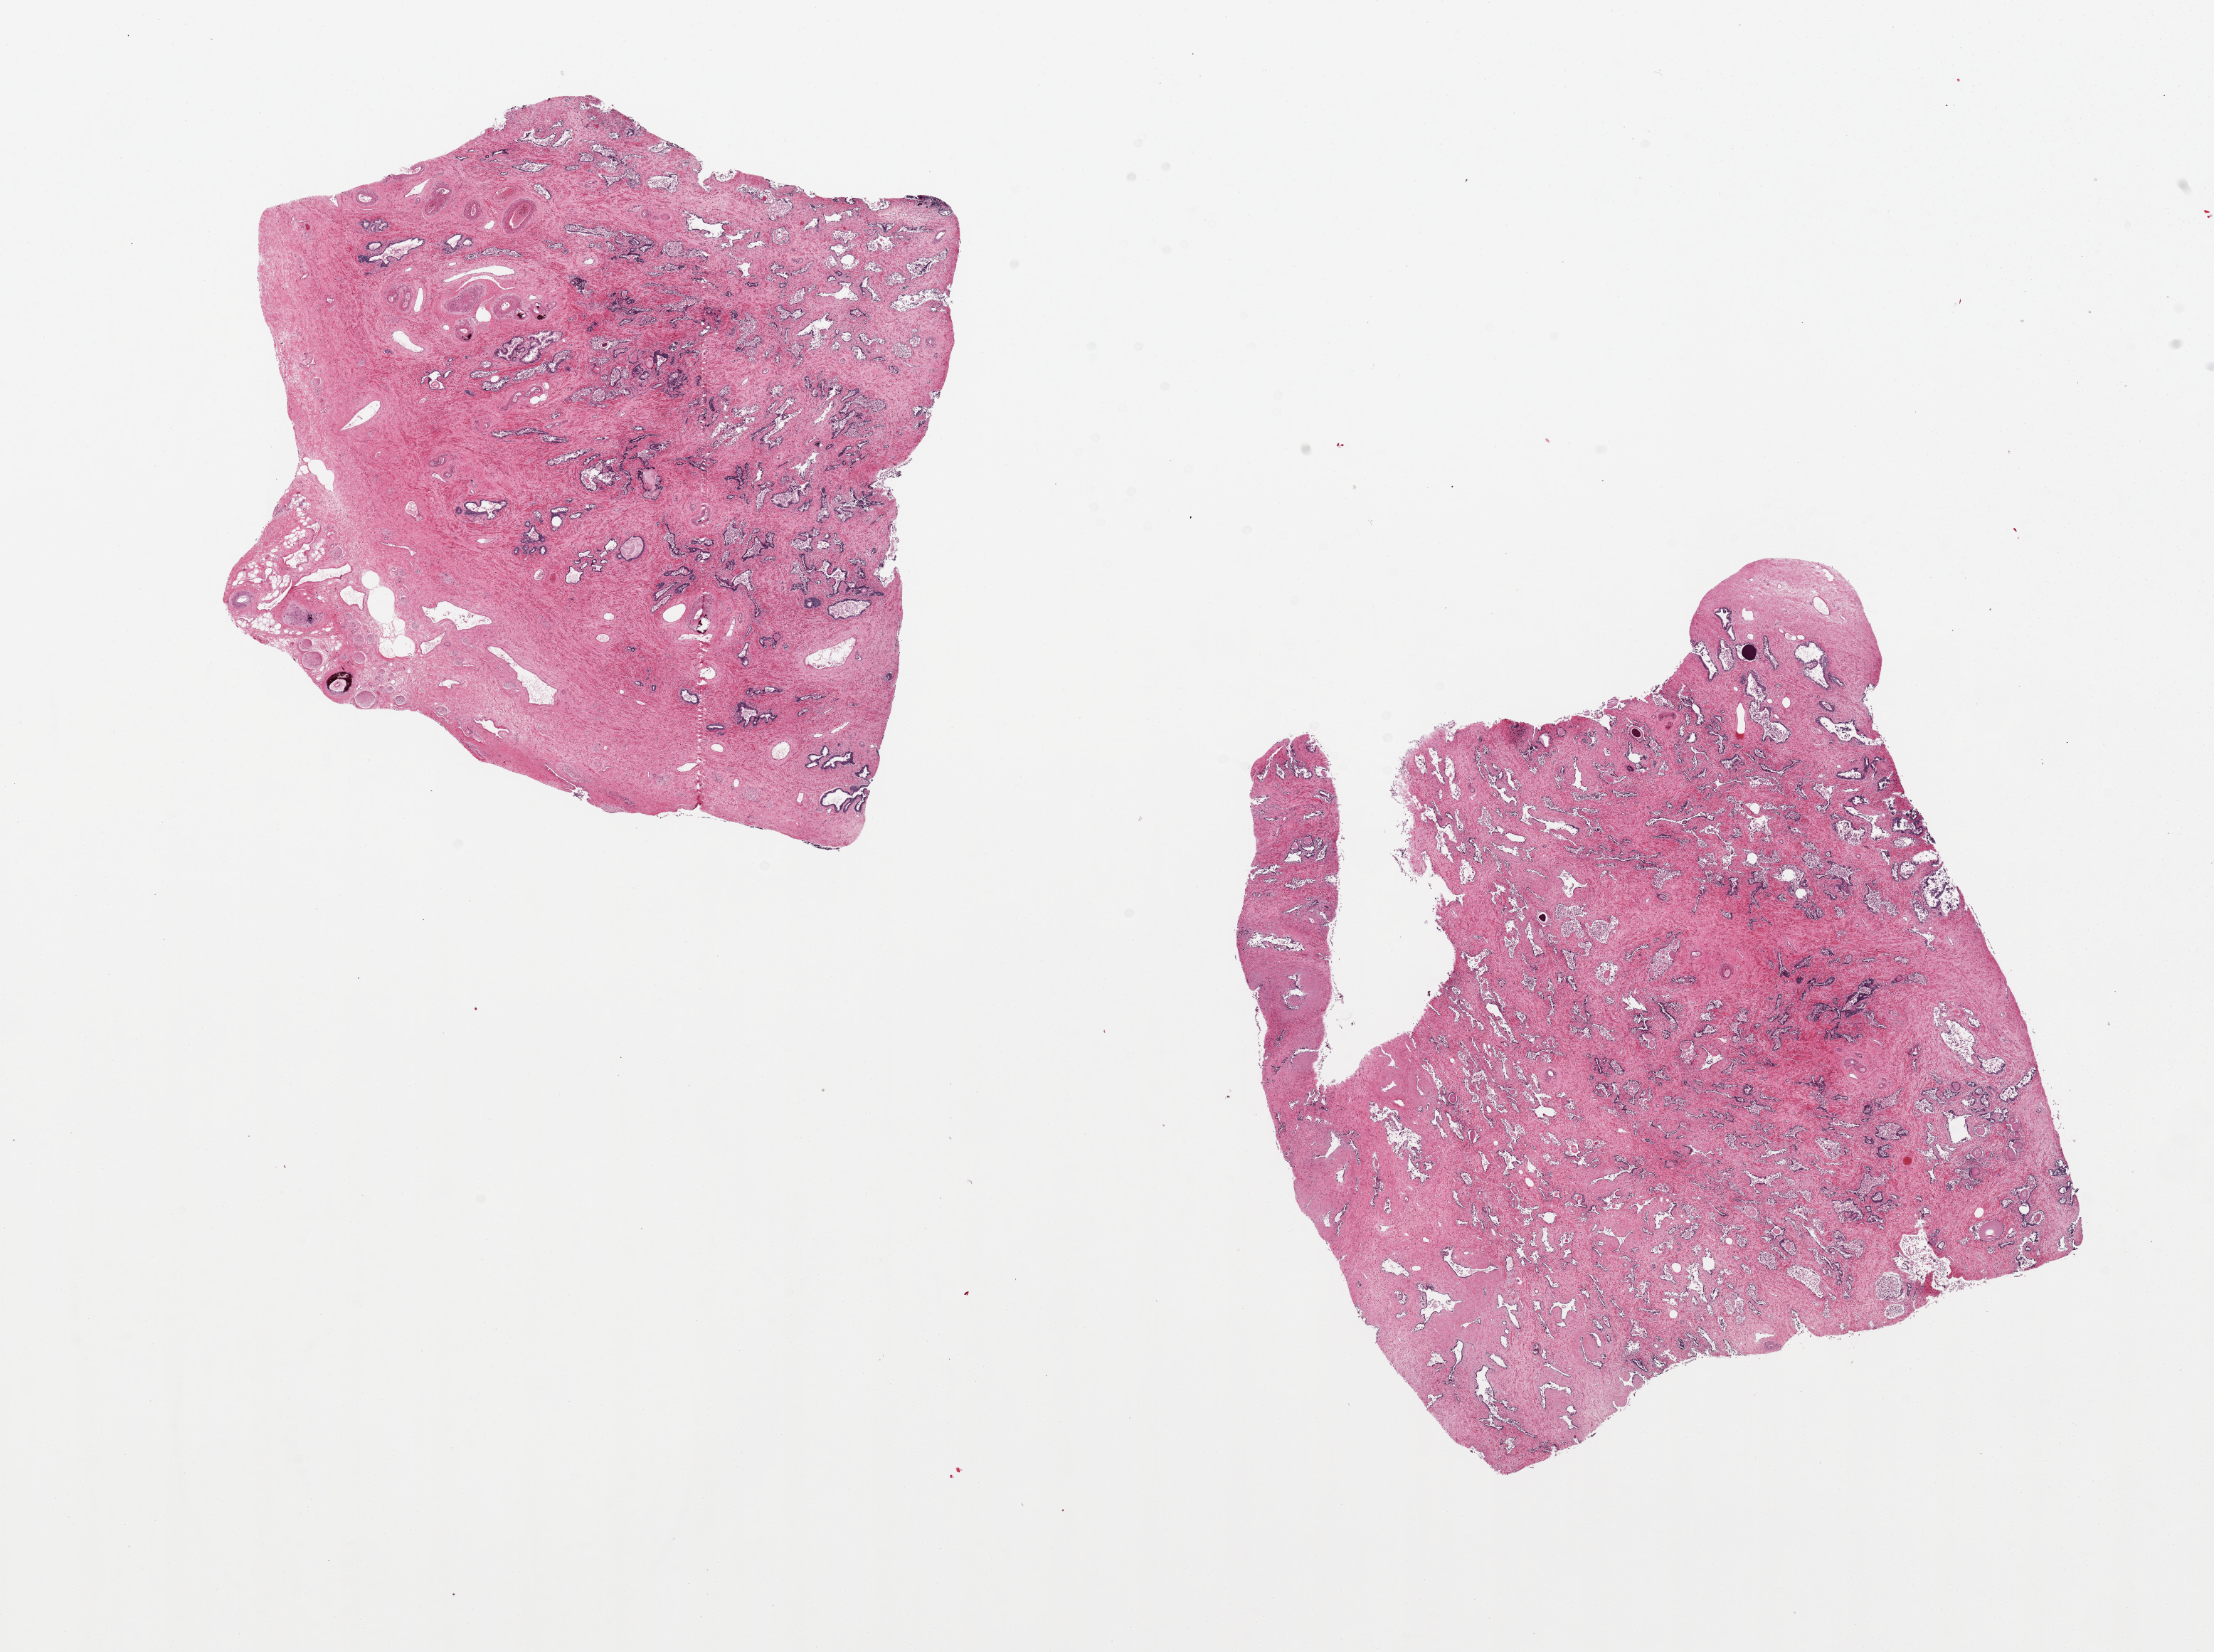
Whole-slide image, hematoxylin and eosin (H&E) stain — low-resolution overview of the scanned area, about 24.6 x 18.4 mm (acquisition: 20x scan); PAXgene-fixed, paraffin-embedded tissue; target tissue: prostate; tissue donor sample. Male donor.
Pathologist's review note for this sample: 2 pieces; atrophy.